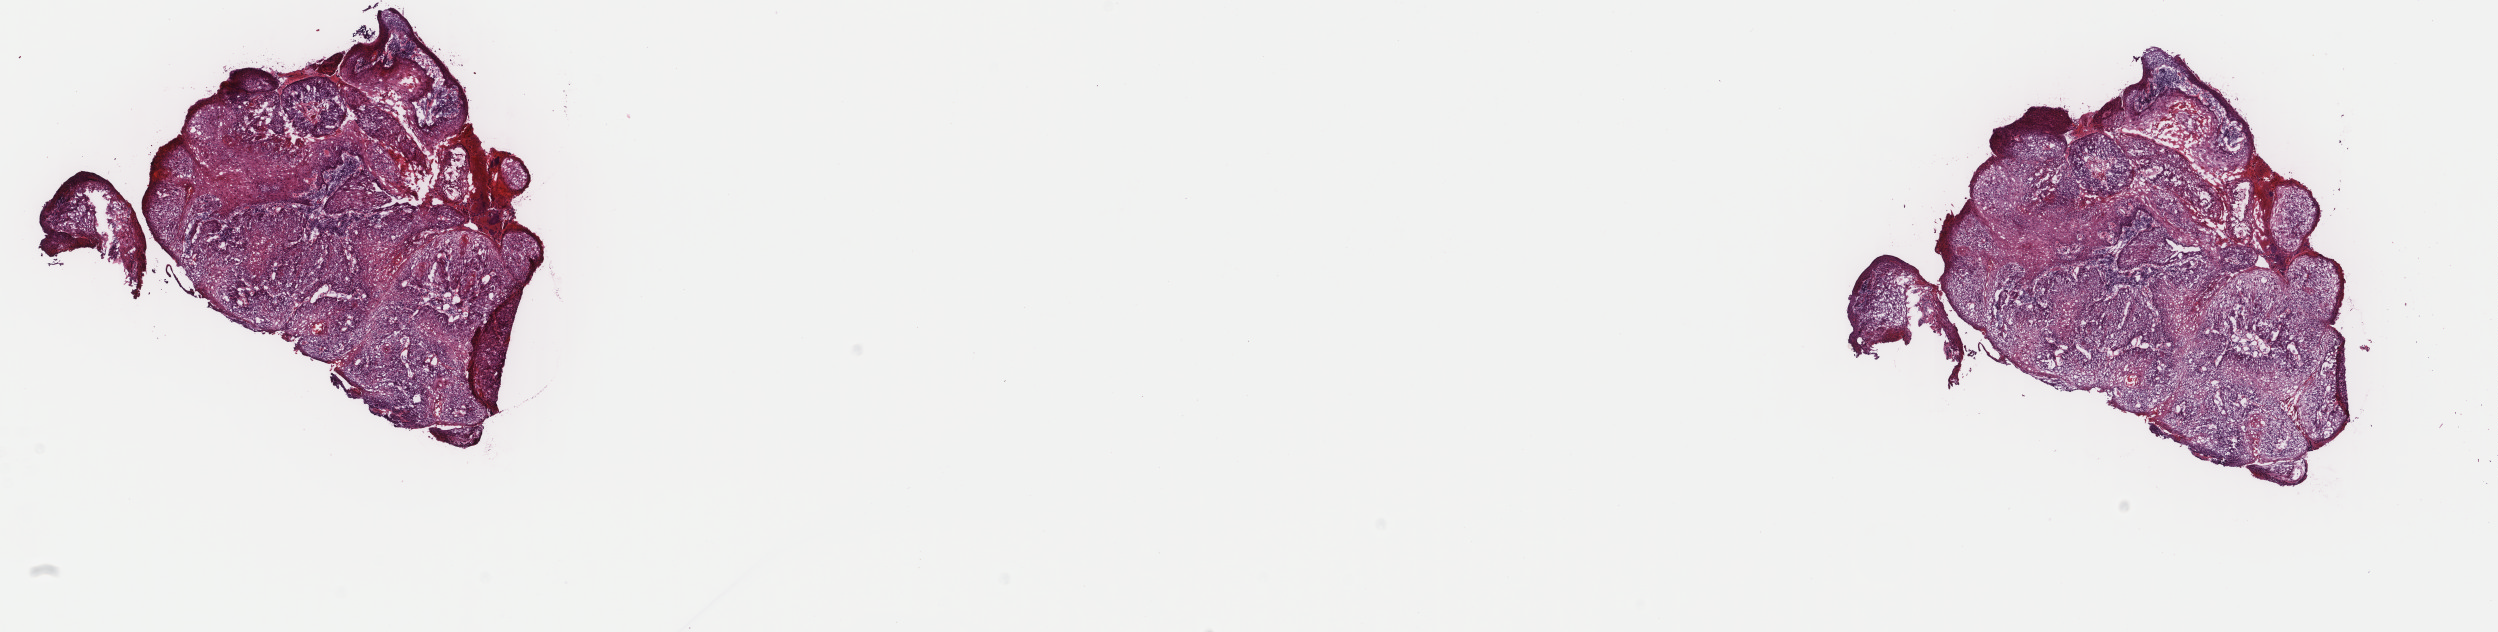
Digitized H&E tissue section (whole slide) — a low-resolution overview of the entire scanned area, about 19.8 x 5.0 mm (acquisition: 40x scan), frozen section, head and neck, primary tumour sample. Patient: male, age at initial diagnosis 61 years. Histologic grade: G3 (poorly differentiated). Composition of this section per pathologist review: tumour cells 90%, tumour nuclei 95%, normal cells 0%, stromal cells 10%, necrosis 0%. Inflammatory infiltration, as recorded: lymphocyte infiltration 0%, monocyte infiltration 0%, neutrophil infiltration 0%.
Diagnosis: Squamous cell carcinoma, NOS (larynx, NOS). TNM: T3 N2b M0. AJCC pathologic stage: IVA (7th edition).